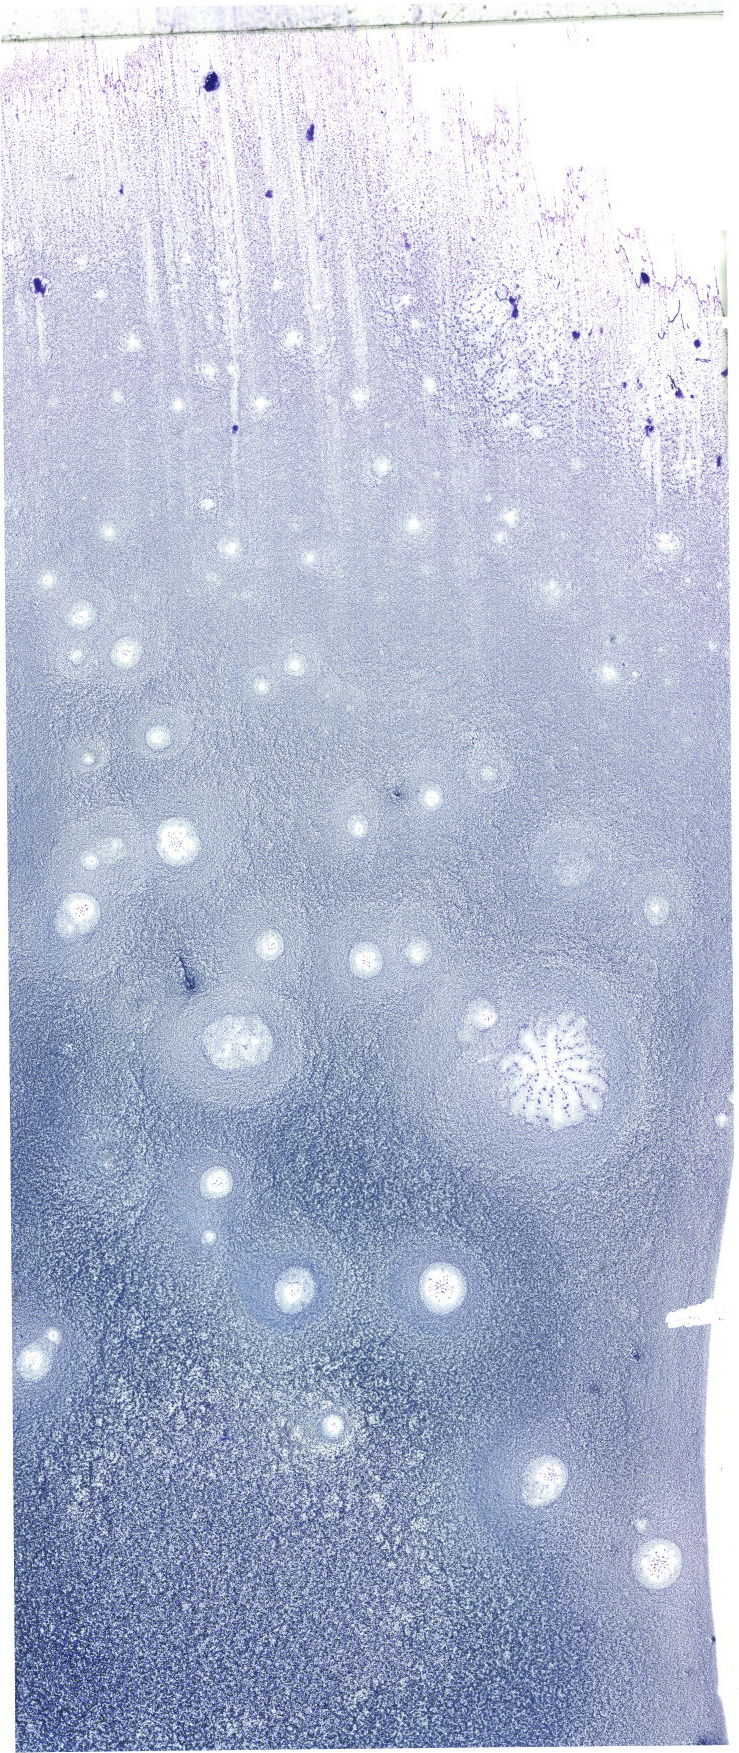
Whole-slide image of a May-Grünwald–Giemsa-stained bone marrow aspirate smear, low-resolution overview of the scanned area, about 20.9 x 49.7 mm. Patient sex: male.
Diagnosis: B Acute Lymphoblastic Leukemia.